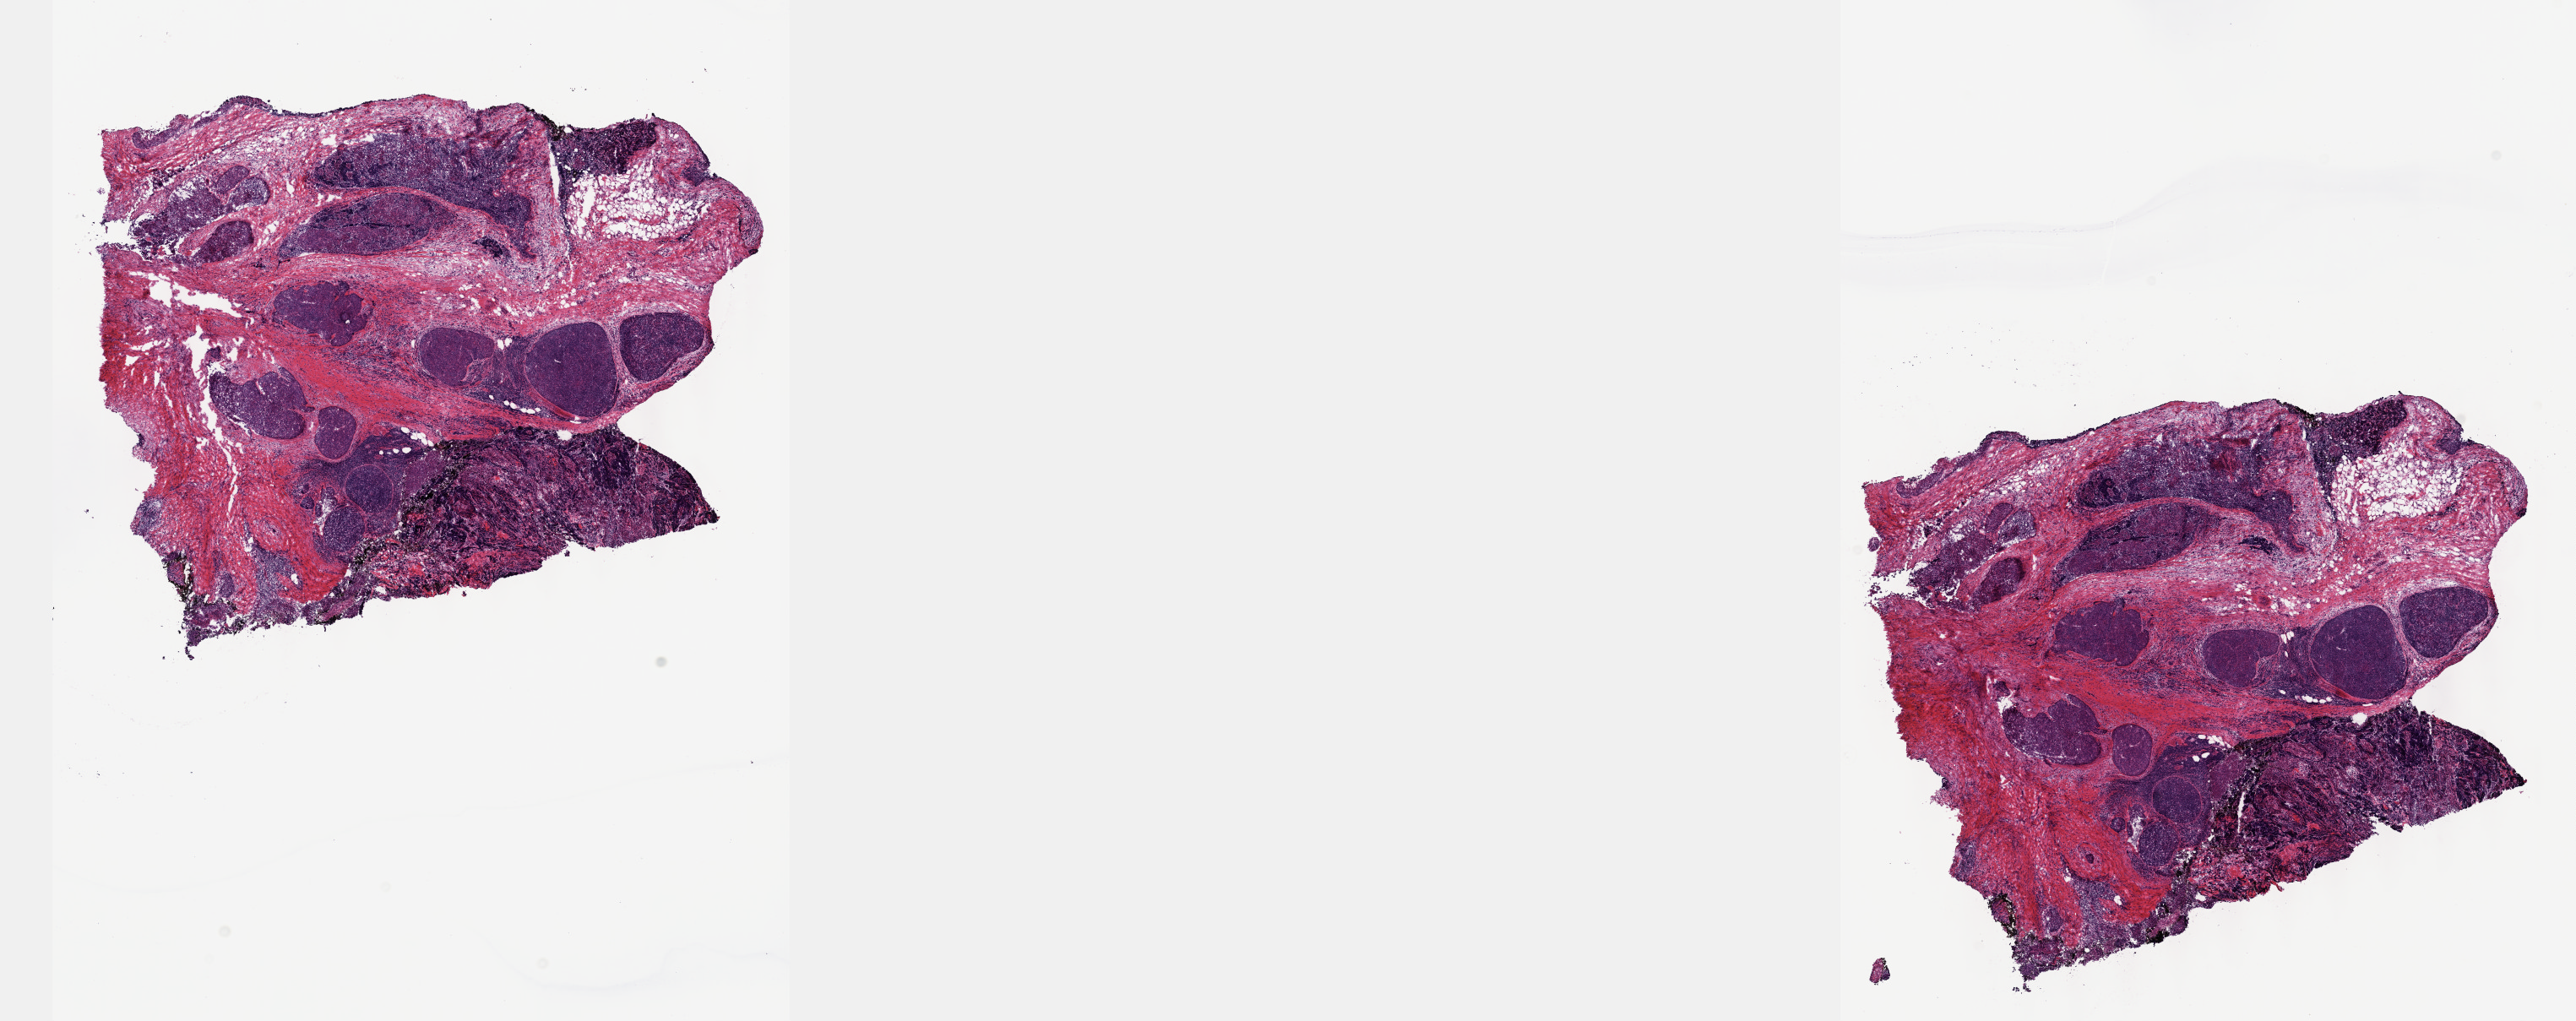
Hematoxylin and eosin (H&E) stained whole-slide image — whole scanned area (about 24.6 x 9.8 mm, acquisition: 40x scan) shown as a low-resolution overview. Frozen section from the top of the tissue portion. Sample: primary tumour, thymus. Male patient; age at initial diagnosis 46 years. Pathologist review of this section (percent, as recorded): tumour cells 60%, tumour nuclei 90%, normal cells 0%, stromal cells 40%, necrosis 0%. Inflammatory infiltration, as recorded: lymphocyte infiltration 0%, monocyte infiltration 0%, neutrophil infiltration 0%.
• histologic diagnosis: Thymoma, type AB, malignant (anterior mediastinum)